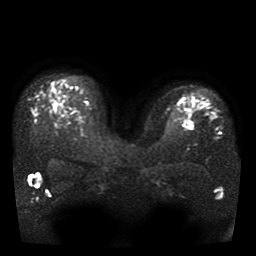
Breast MRI, one axial slice. Slice 28 of 41 in the series (ordered by position). Diffusion-weighted series; image 2 of 4 stored at this slice position (different b-values; order by instance number). 1.5 T. 5 mm slice thickness. 256 × 256 image matrix. Female patient.
Outlined on this slice (expert manual segmentation):
- tumour on diffusion-weighted imaging: bounding box (x1, y1, x2, y2) in pixels: (188, 122, 194, 126)